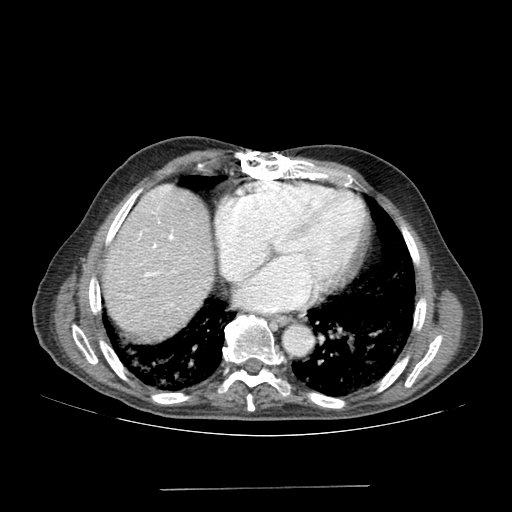
Contrast-enhanced abdominal CT (liver protocol), one axial slice; slice 166 of 192 in the series (ordered by position); 120 kVp; soft-tissue window (W 400 / L 40 HU); 2.5 mm slice thickness; 512 × 512 image matrix, field of view 400 × 400 mm. From the clinical record (not read from this slice): diagnosis: hepatocellular carcinoma (patient treated with transarterial chemoembolisation; whether this scan precedes or follows treatment is not stated here); TNM stage (as recorded): Stage-IVA; Child-Pugh class: A; tumour differentiation: poorly differentiated; tumour nodularity: uninodular.
Annotated regions visible in this slice (semi-automatic segmentation, software-assisted and operator-edited):
- liver parenchyma outside the tumour (the mass and vessels are separate outlines, so this box may not span the whole liver): bounding box (x1, y1, x2, y2) in pixels: (102, 184, 214, 338)
- liver vessels: (128, 187, 174, 298)